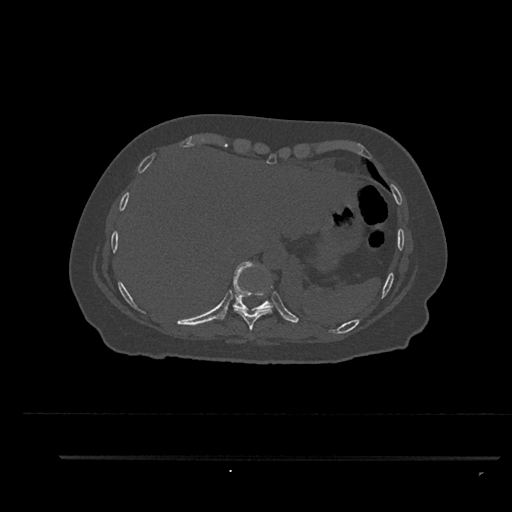
CT including the spine, one axial slice. Slice 393 of 797 in the series (ordered by position). 120 kVp. Bone window (W 1800 / L 400 HU). 0.5 mm slice thickness. 512 × 512 image matrix. Patient: female, 44 years. Case-level facts recorded for this patient, not image findings: primary cancer: renal; vertebrae with lytic lesions (as recorded): L1.
Structures marked on this image (semi-automatically segmented with operator editing):
- T10 vertebra: bounding box (x1, y1, x2, y2) in pixels: (220, 260, 274, 320)
- T9 vertebra: (234, 308, 273, 331)